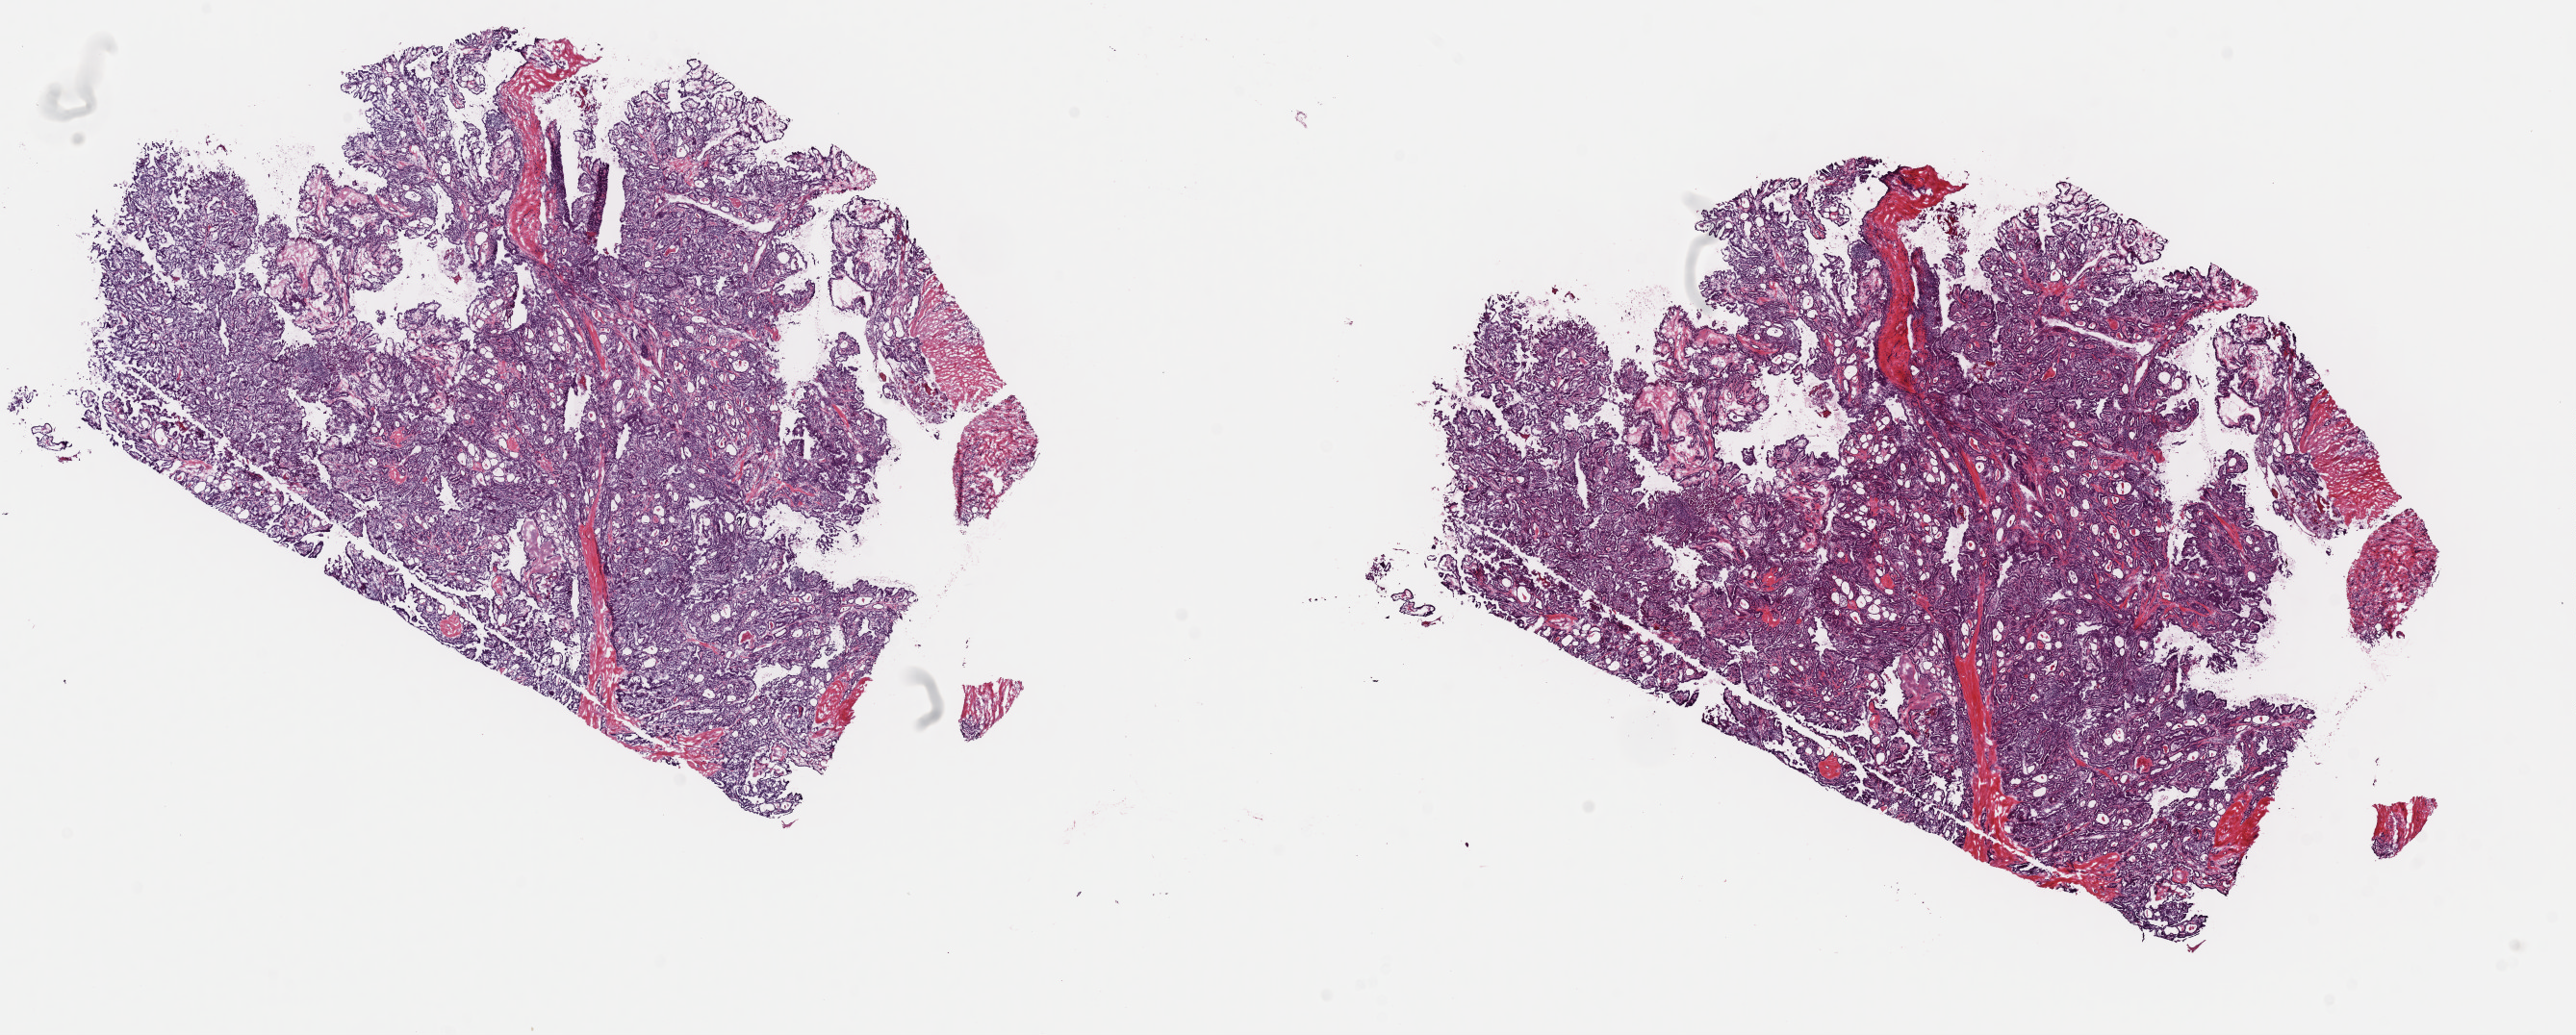
Hematoxylin and eosin (H&E) stained whole-slide image, low-resolution overview of the scanned area, about 21.1 x 8.5 mm; frozen section; sample: primary tumour, thyroid. Female, age 38 years at initial diagnosis. Pathologist review of this section (percent, as recorded): tumour cells 90%, tumour nuclei 90%, normal cells 0%, stromal cells 10%, necrosis 0%. Inflammatory infiltration, as recorded: lymphocyte infiltration 1%, monocyte infiltration 0%, neutrophil infiltration 0%.
• diagnosis: Papillary adenocarcinoma, NOS (thyroid gland)
• laterality: right
• AJCC pathologic stage: I
• TNM: T1 N0 M0